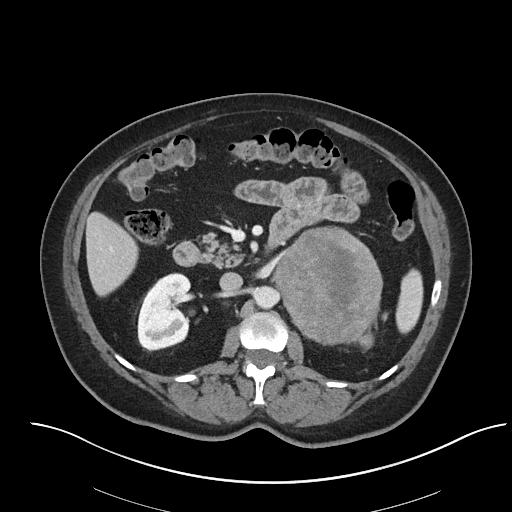
Contrast-enhanced abdominal CT, one axial slice. Position 37 of 92 along the scan axis. Reconstruction kernel I40f/2. Intravenous contrast given. Soft-tissue window (W 400 / L 40 HU). 3 mm slice thickness. 512 × 512 image matrix, field of view 440 × 440 mm. Patient: female, 53 years. From the clinical record (not read from this slice): diagnosis: adrenocortical carcinoma; tumour side: left adrenal; tumour size at pathology: 9 cm; Ki-67 index: 28 %; stage (as recorded): 2.
Annotated regions visible in this slice (semi-automatically segmented with operator editing):
- mass: bounding box (x1, y1, x2, y2) in pixels: (276, 228, 381, 343)